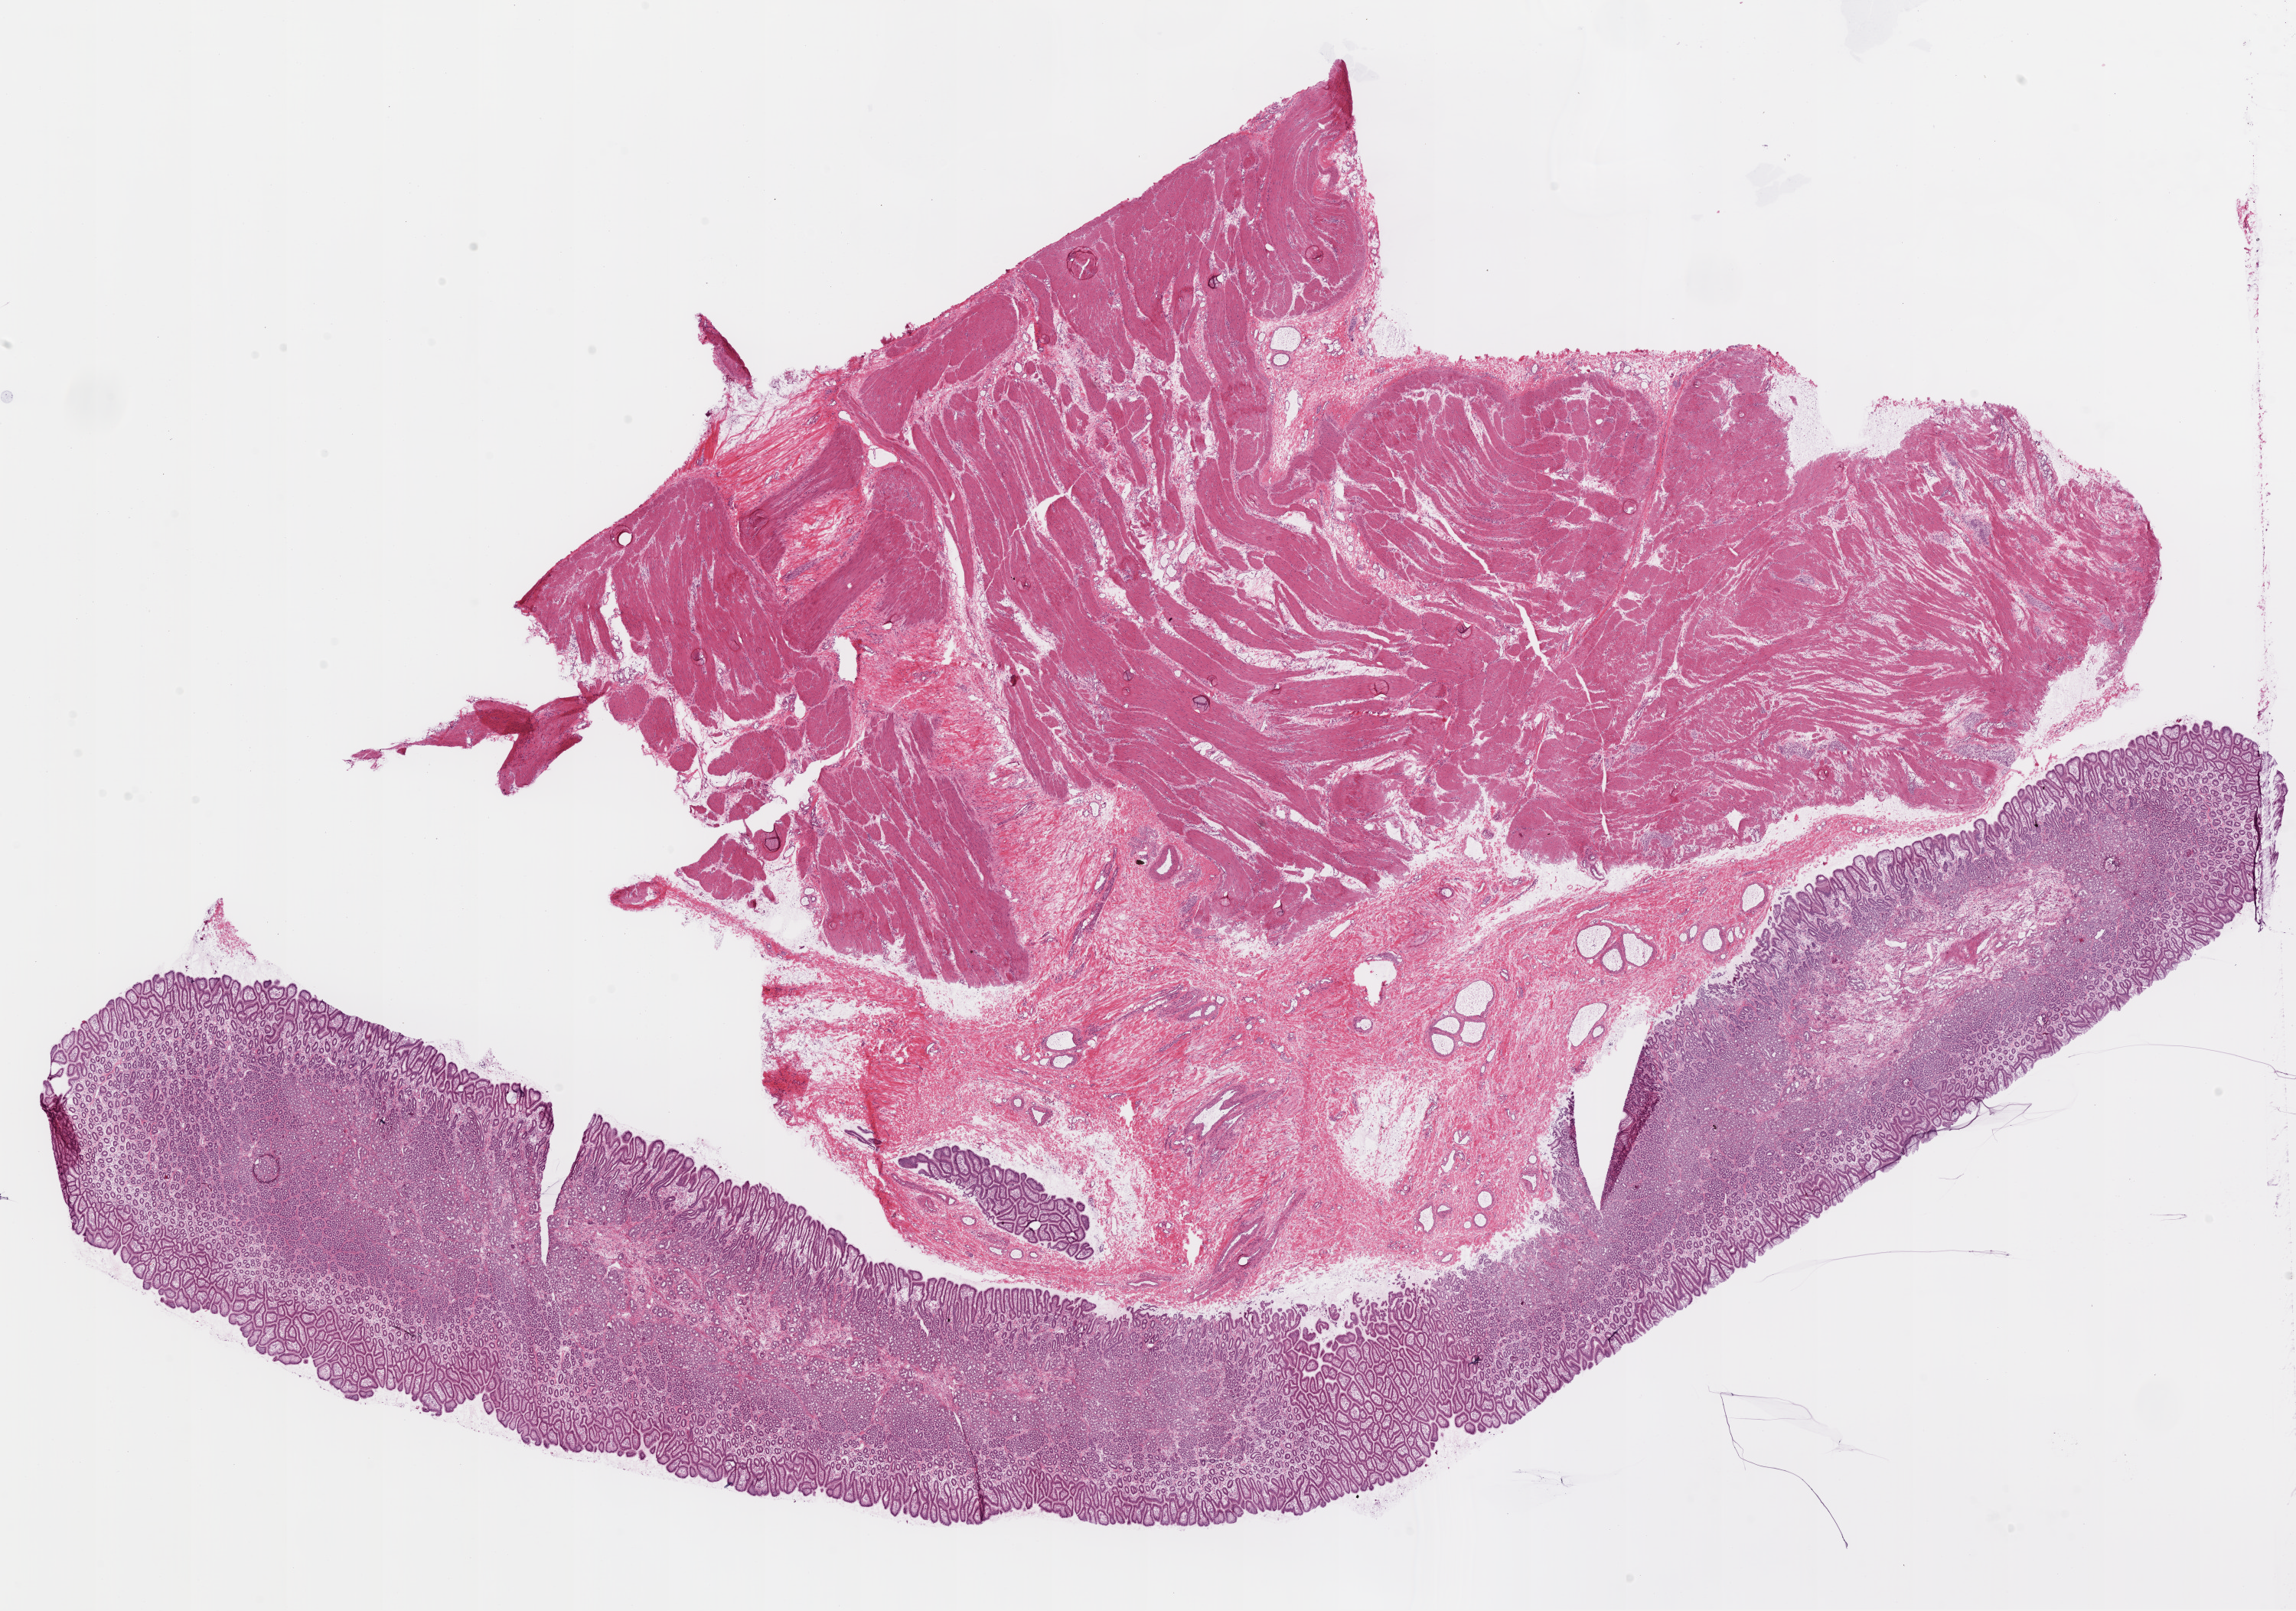
H&E-stained whole-slide image — a low-resolution overview of the entire scanned area, about 24.1 x 16.9 mm. Frozen section from the top of the tissue portion. Sample: solid tissue normal (non-tumour tissue), stomach. Patient: female, age at initial diagnosis 53 years.
This section: solid tissue normal (non-tumour) sample from the same patient. Patient diagnosis: Adenocarcinoma, NOS (cardia, NOS).